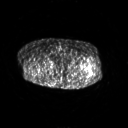
FDG PET of an extremity soft-tissue mass (from a PET/CT study), one axial slice. Position 257 of 267 along the scan axis. 3.27 mm slice thickness. 128 × 128 image matrix, field of view 700 × 700 mm. Female patient, age 62 years. Case-level facts recorded for this patient, not image findings: histological type: undifferentiated – high grade; grade: high; site of the primary tumour: left thigh.
Outlined on this slice (expert contour drawn on MRI and transferred to this co-registered scan by the dataset authors):
- gross tumour volume including surrounding oedema: bounding box [x1, y1, x2, y2] px = [87, 68, 94, 78]
- gross tumour volume (mass): [89, 73, 92, 75]